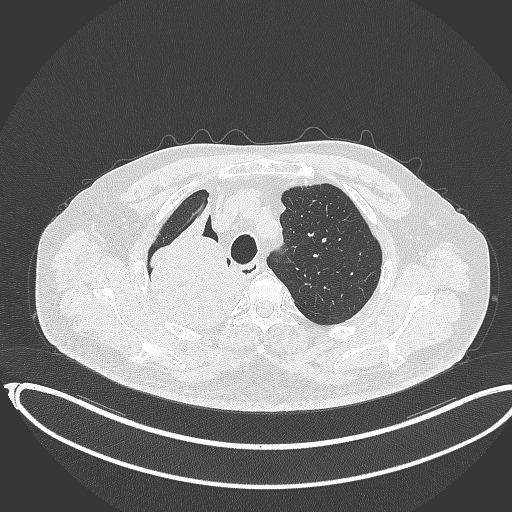
Chest CT, one axial slice; position 296 of 403 along the scan axis; 120 kVp; lung window (W 1500 / L -600 HU); 1 mm slice thickness; 512 × 512 image matrix, field of view 436 × 436 mm. Patient: male, 68 years. From the clinical record (not read from this slice): clinical TNM (as recorded): T2a N0 M0.
Outlined on this slice (rectangle marked by the reading radiologist):
- lung tumour (recorded histology: adenocarcinoma): bounding box [x1, y1, x2, y2] px = [136, 204, 244, 330]